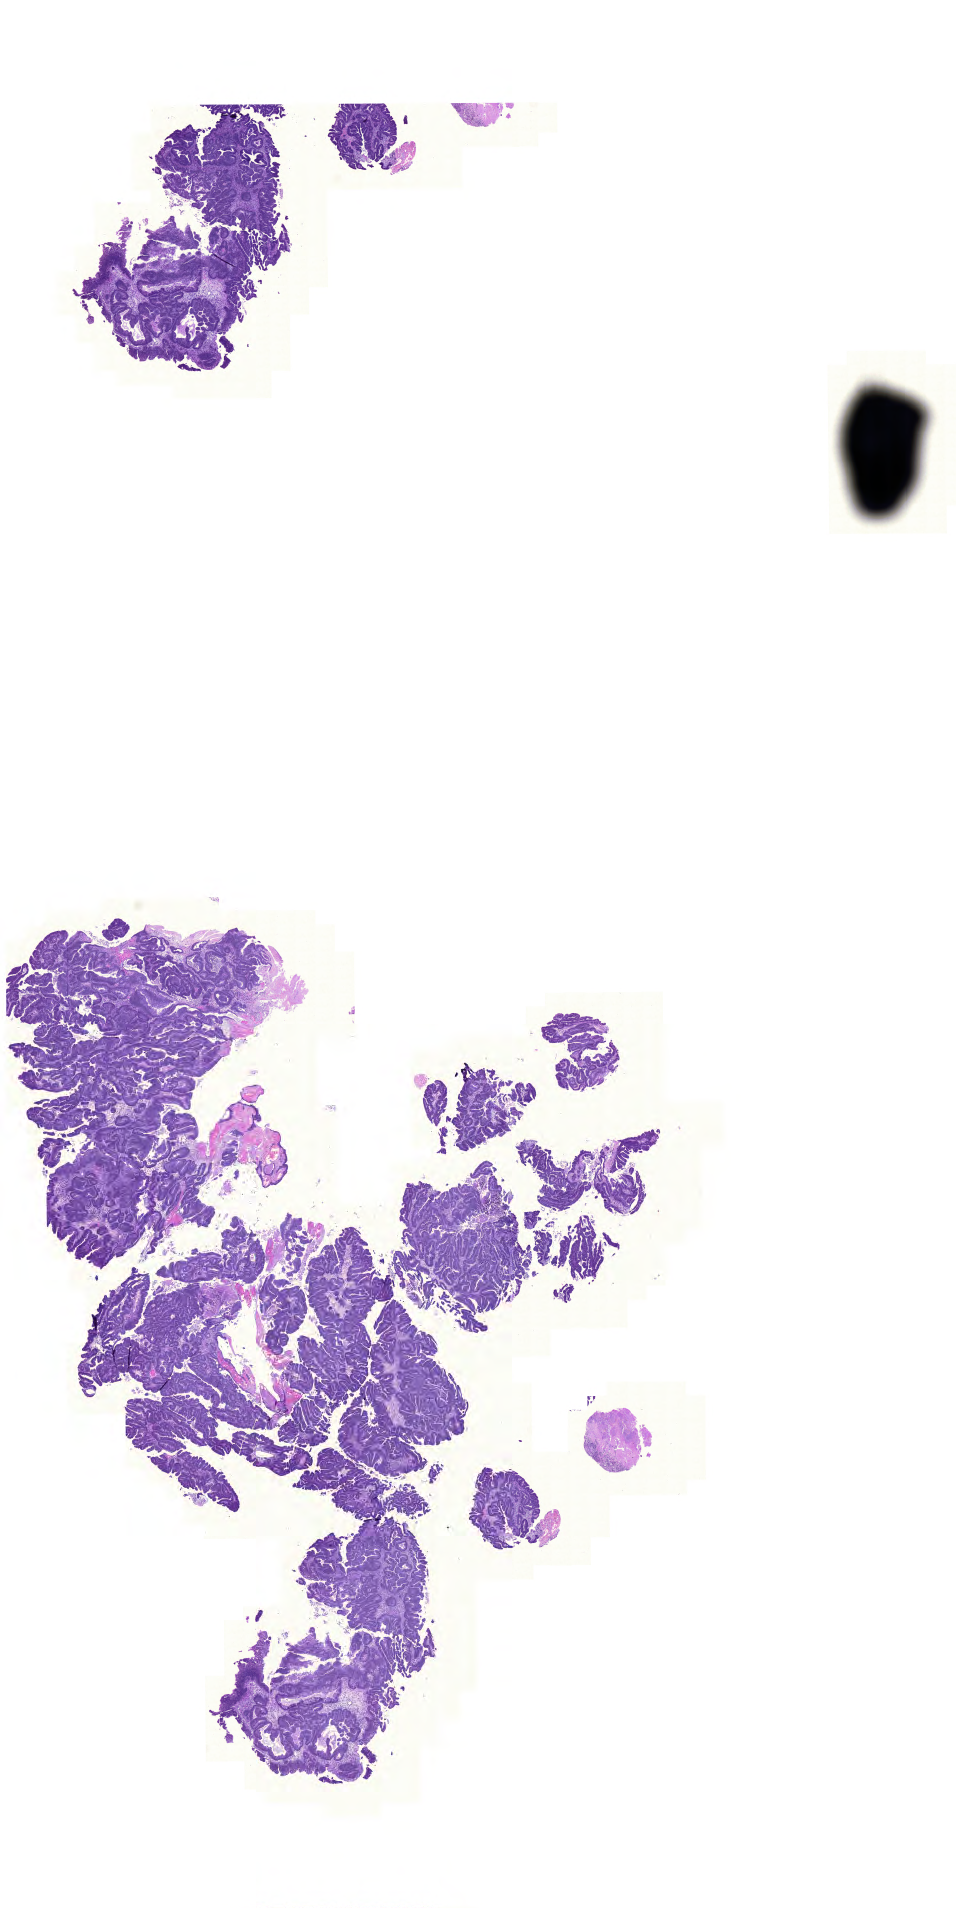
Hematoxylin and eosin (H&E) stained whole-slide image, shown as a low-resolution overview of the whole scanned area (about 14.2 x 28.4 mm). Formalin-fixed paraffin-embedded (FFPE) diagnostic section. Sample: primary tumour, colon. Male, age 80 years at initial diagnosis.
• pathologic diagnosis: Adenocarcinoma, NOS (ascending colon)
• AJCC pathologic stage: I (6th edition)